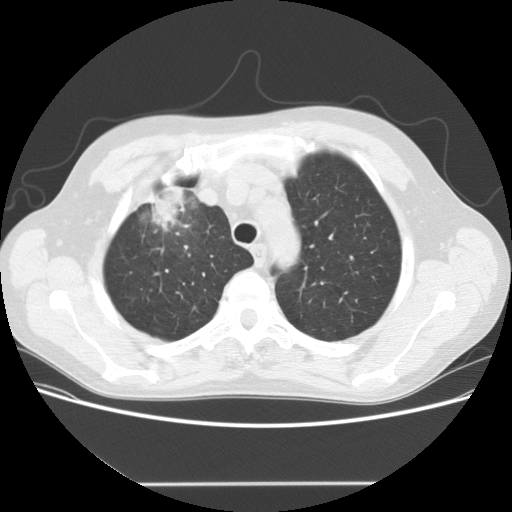
Low-dose screening chest CT, one axial slice. Position 124 of 153 along the scan axis. 120 kVp. Lung window (W 1500 / L -600 HU). 2.5 mm slice thickness. 512 × 512 image matrix, field of view 360 × 360 mm.
Outlined on this slice (expert manual segmentation):
- lesion 1 (tumor, upper lobe of right lung): box from (x=151, y=185) to (x=188, y=232) px